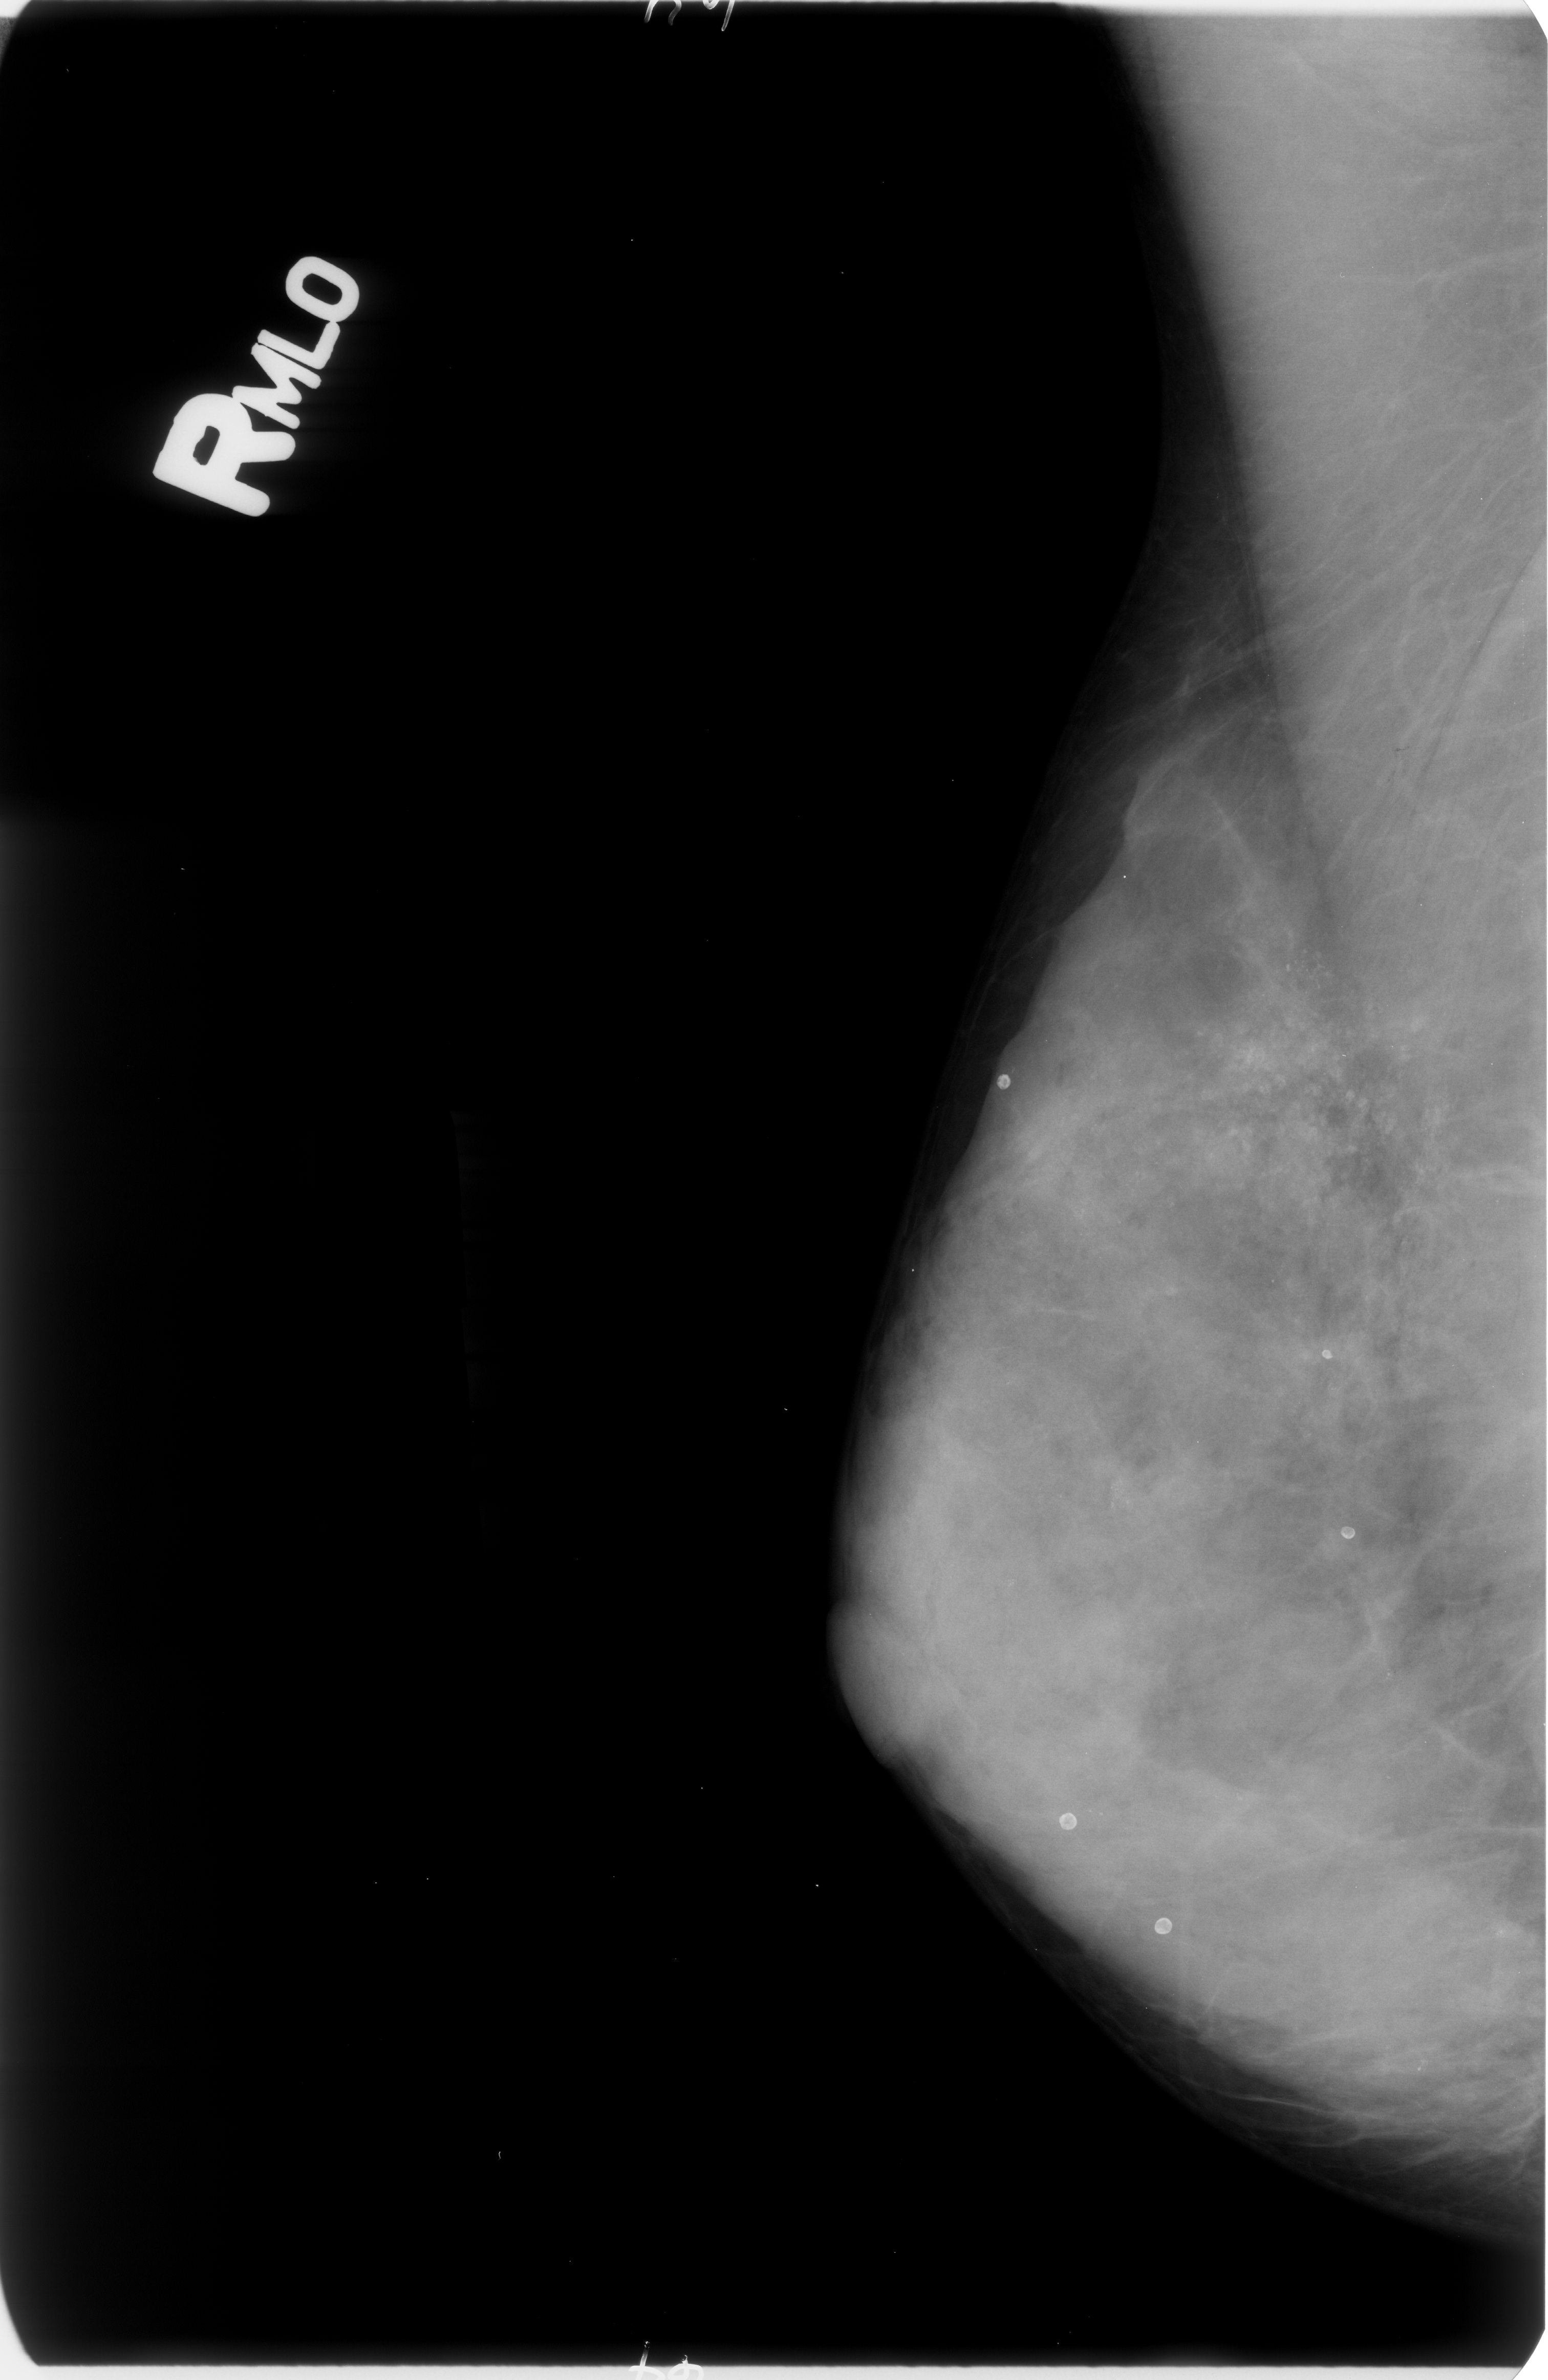
Scanned film-screen mammogram; right breast; MLO view; BI-RADS breast density category 4 (scale 1–4).
Finding: calcifications, morphology punctate / amorphous, distribution regional; BI-RADS assessment category 4; subtlety rating 4 on a 1 (subtle) to 5 (obvious) scale; pathology result (as recorded, not read from the image): benign.